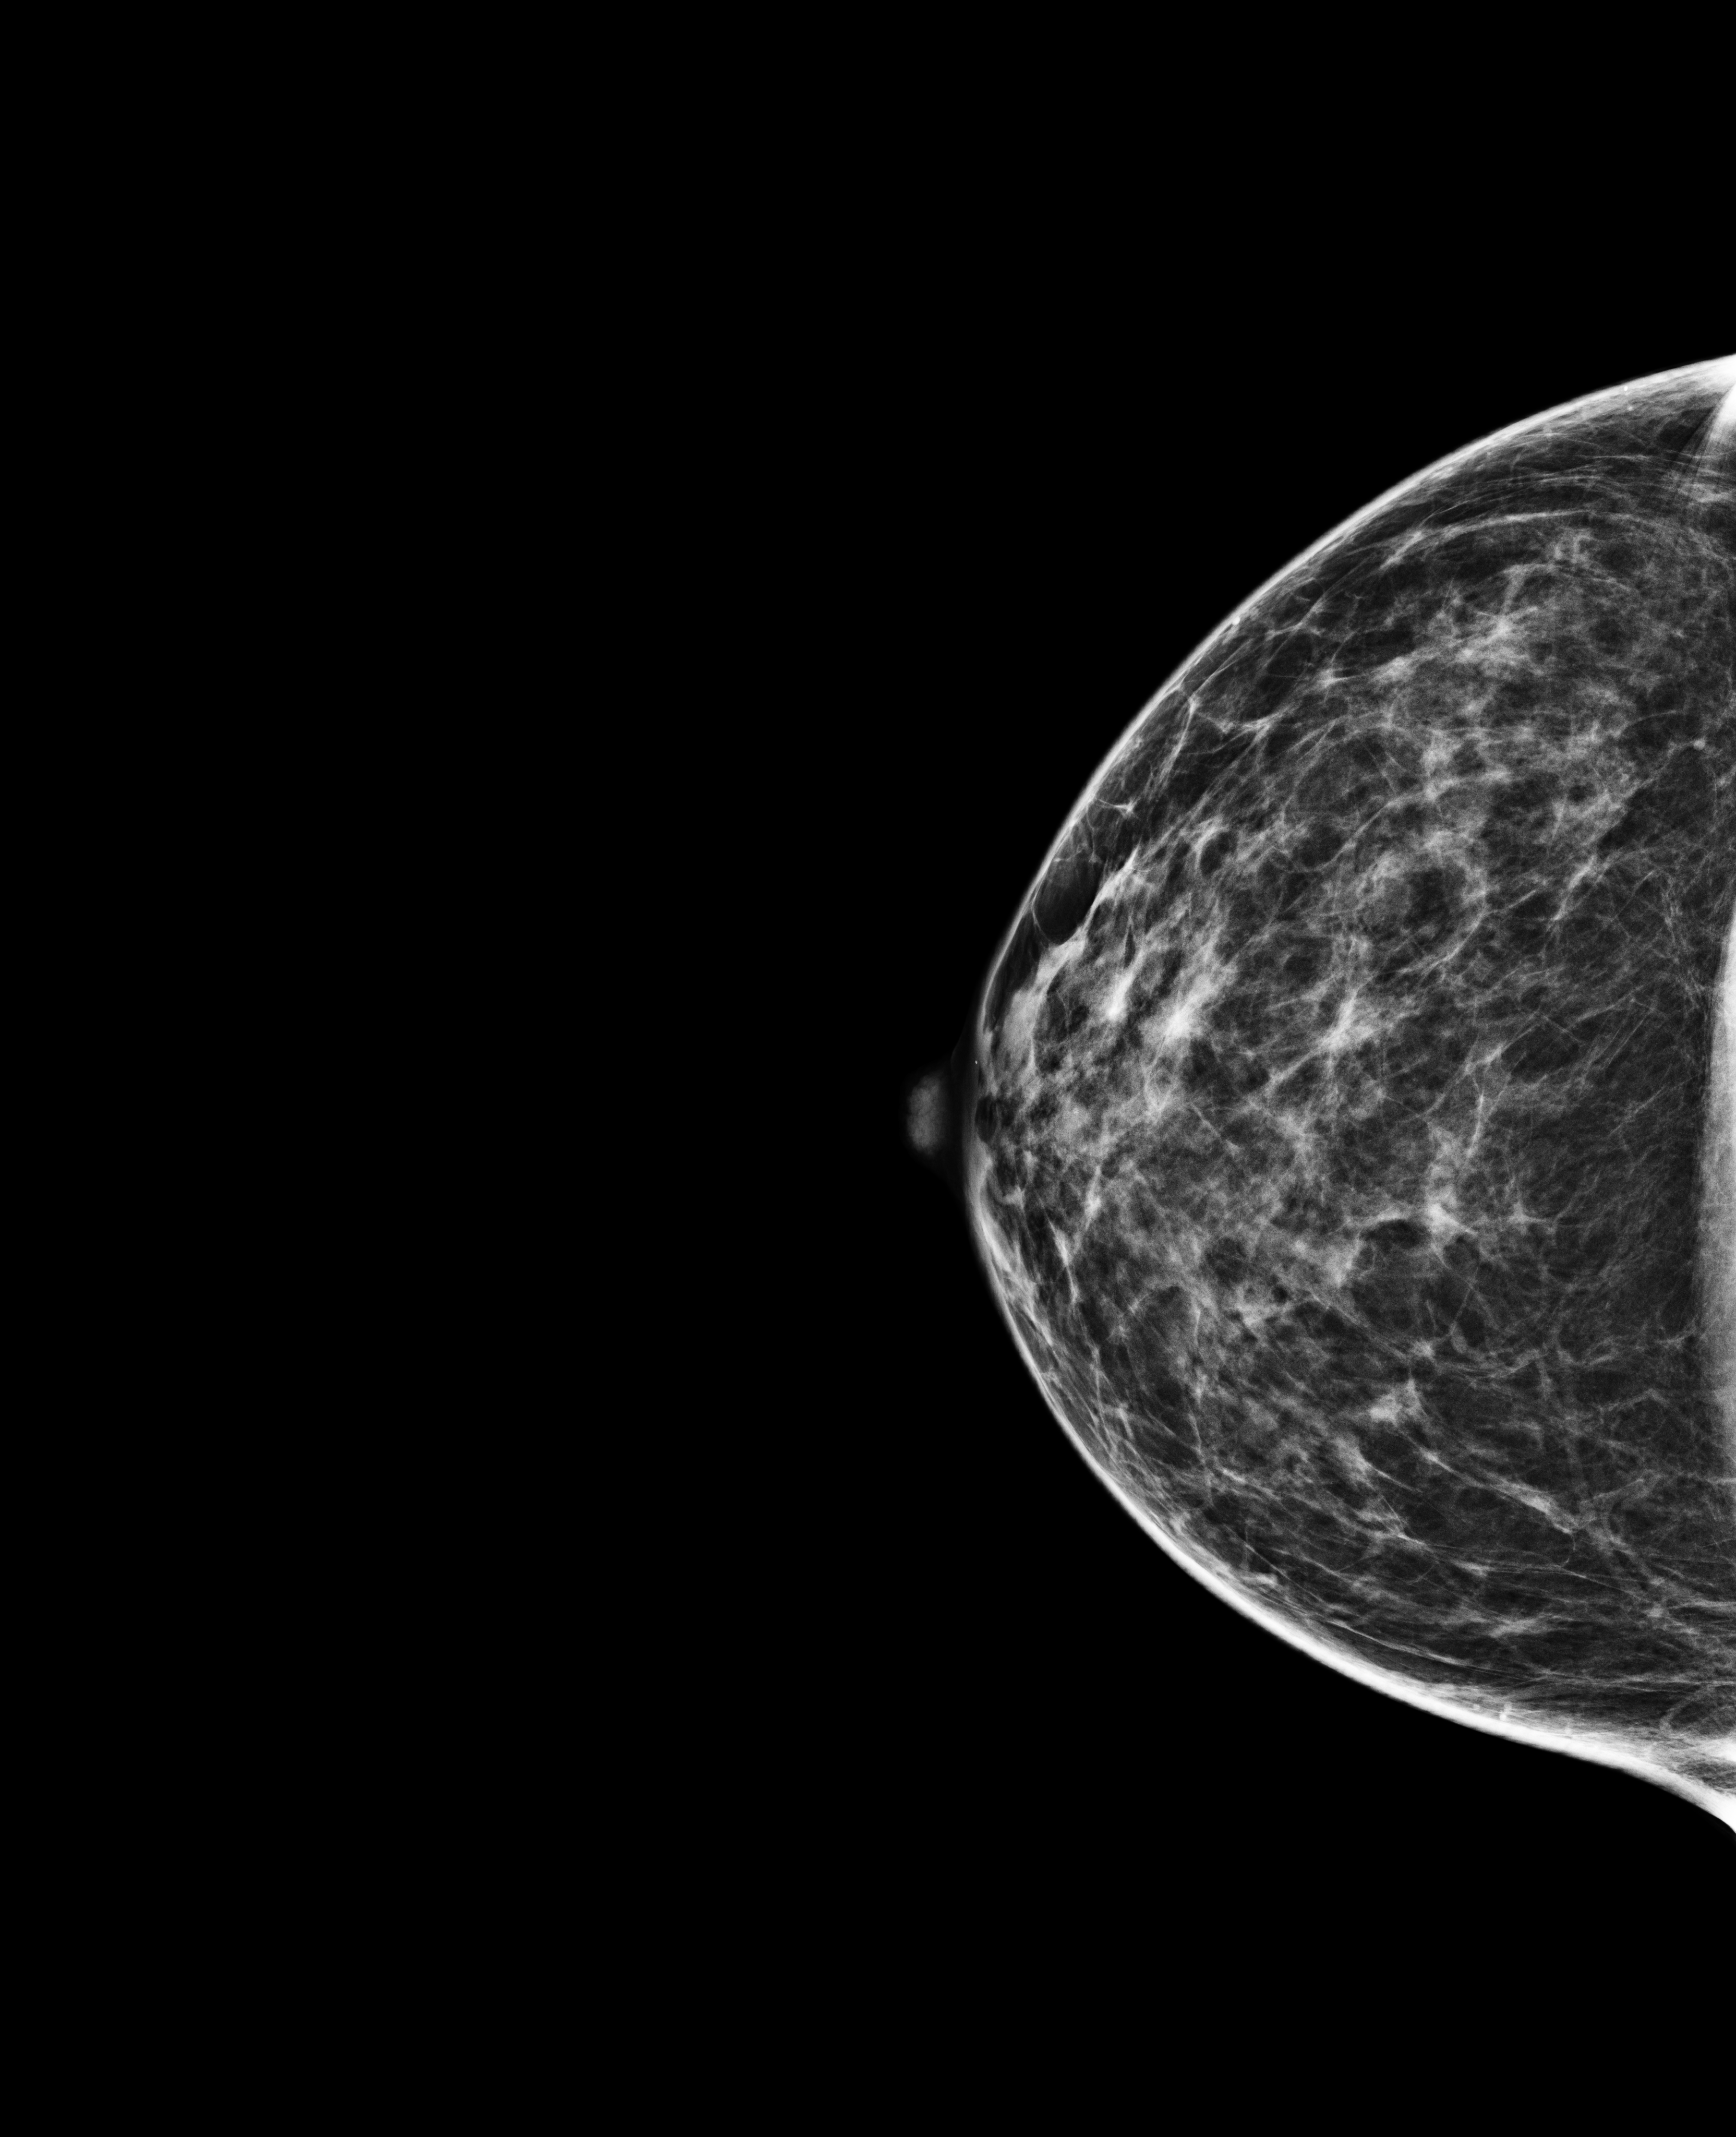
Full-field digital mammogram (FFDM); right breast; craniocaudal (CC) view; screening examination. Patient aged 48 years (female).
- BI-RADS breast density category at the screening exam (both breasts, scale 1–4): 2
- final BI-RADS assessment for this screening round (tomosynthesis exam, both breasts): category 1
- recall: no recall after this screen